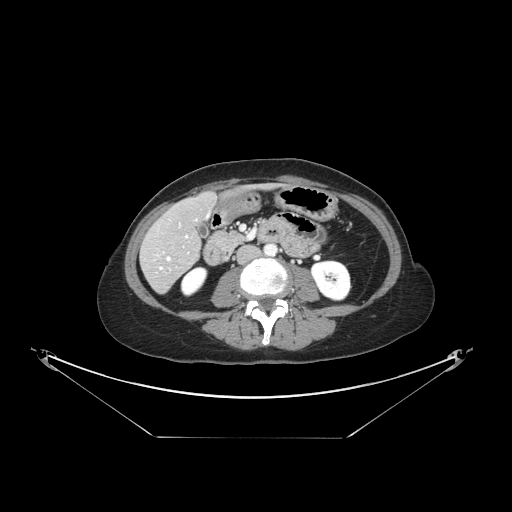
Contrast-enhanced abdominal CT, one axial slice. Slice 45 of 148 in the series (ordered by position). 120 kVp. Intravenous contrast given. Soft-tissue window (W 400 / L 40 HU). 2.5 mm slice thickness. 512 × 512 image matrix, field of view 500 × 500 mm. Female patient, age 73 years. Case-level facts recorded for this patient, not image findings: diagnosis: colorectal cancer liver metastases, imaged before liver resection; multiple liver metastases: no; largest metastasis: 1 cm; disease in both lobes: no.
Structures marked on this image (expert manual segmentation):
- hepatic veins: box from (x=157, y=236) to (x=188, y=269) px
- liver: (x=143, y=194)–(x=216, y=292)
- planned liver remnant (the part of the liver to remain after resection): (x=161, y=195)–(x=216, y=243)